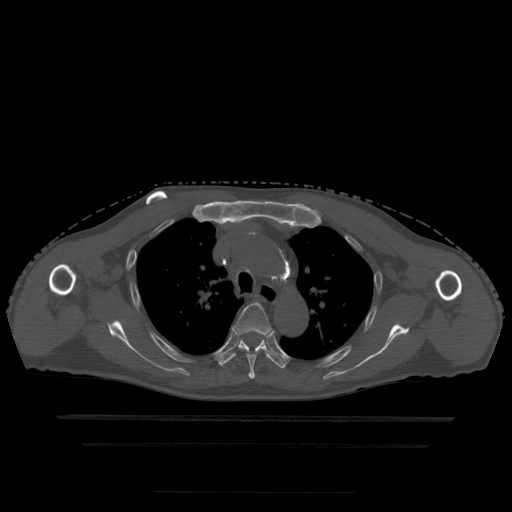
CT including the spine, one axial slice. Slice 347 of 522 in the series (ordered by position). Bone window (W 1800 / L 400 HU). 1.25 mm slice thickness. 512 × 512 image matrix. Patient age 68 years. From the clinical record (not read from this slice): primary cancer: urothelial.
Annotated regions visible in this slice (semi-automatically segmented with operator editing):
- T4 vertebra: box from (x=234, y=303) to (x=272, y=379) px
- T5 vertebra: (x=219, y=334)–(x=286, y=369)